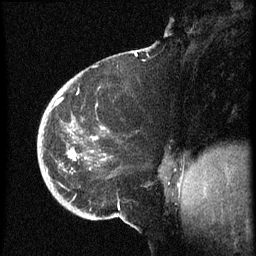
Breast MRI (dynamic contrast-enhanced), one sagittal slice. Slice 20 of 60 in the series (ordered by position). Dynamic contrast-enhanced series, image 2 of 3 at this slice position (ordered by acquisition). 1.5 T. TE 4.2 ms, TR 8.4 ms. 2.5 mm slice thickness. 256 × 256 image matrix, field of view 200 × 200 mm. Female patient, age 38 years. Case-level facts recorded for this patient, not image findings: setting: breast cancer imaged before/during neoadjuvant chemotherapy; receptor status: HER2-positive.
Structures marked on this image (semi-automatically segmented with operator editing):
- analysis volume of interest (the breast-tissue region the enhancement analysis was run in; not a lesion): box from (x=38, y=74) to (x=173, y=202) px
- tumour enhancement mask (voxels above the 70 % enhancement threshold inside the analysis volume of interest): (x=56, y=100)–(x=106, y=162)